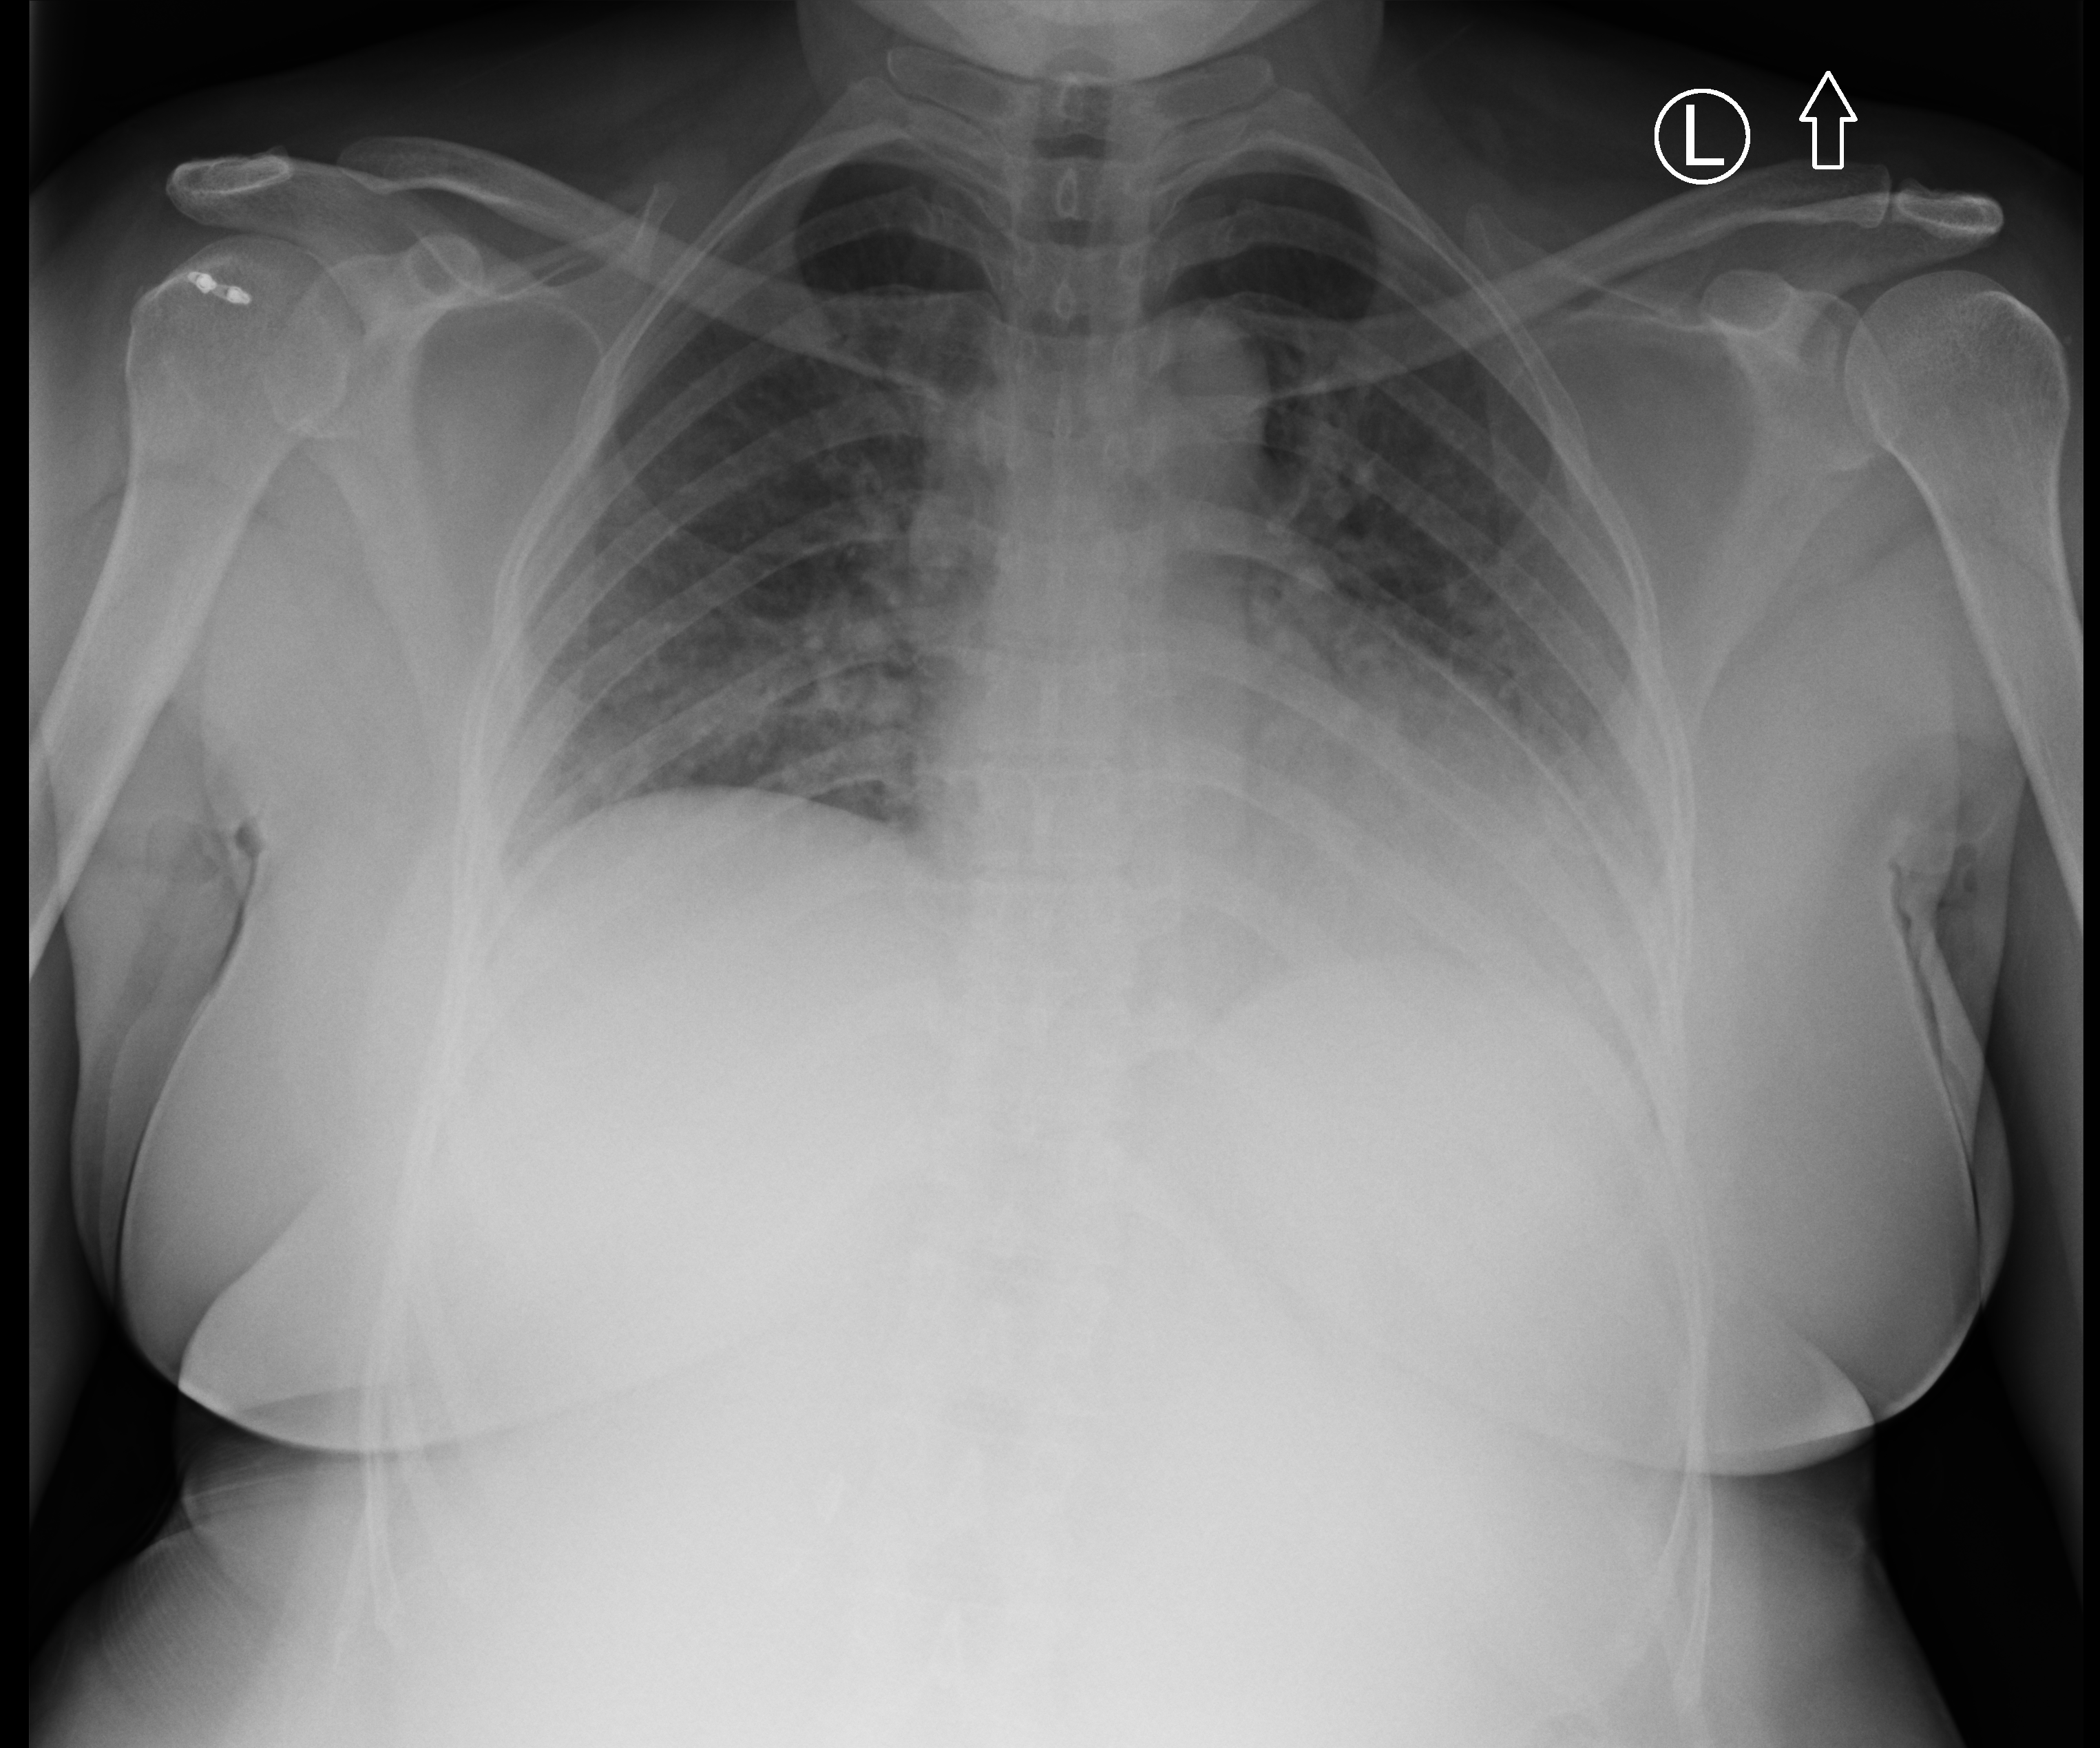
Portable chest radiograph; anteroposterior (AP) projection. Female patient hospitalised with COVID-19, age 18–59 years.
Admission-level facts for this patient (not findings on this image; timing relative to this image not recorded): mechanically ventilated during this hospital stay: no.